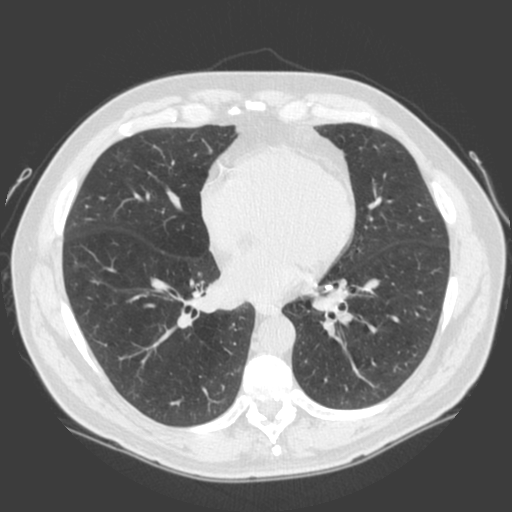
Low-dose screening chest CT, one axial slice; position 81 of 185 along the scan axis; 120 kVp; lung window (W 1500 / L -600 HU); 512 × 512 image matrix.
Annotated regions visible in this slice (expert manual segmentation):
- lesion 1 (tumor, lower lobe of left lung): bounding box (x1, y1, x2, y2) in pixels: (291, 124, 321, 147)